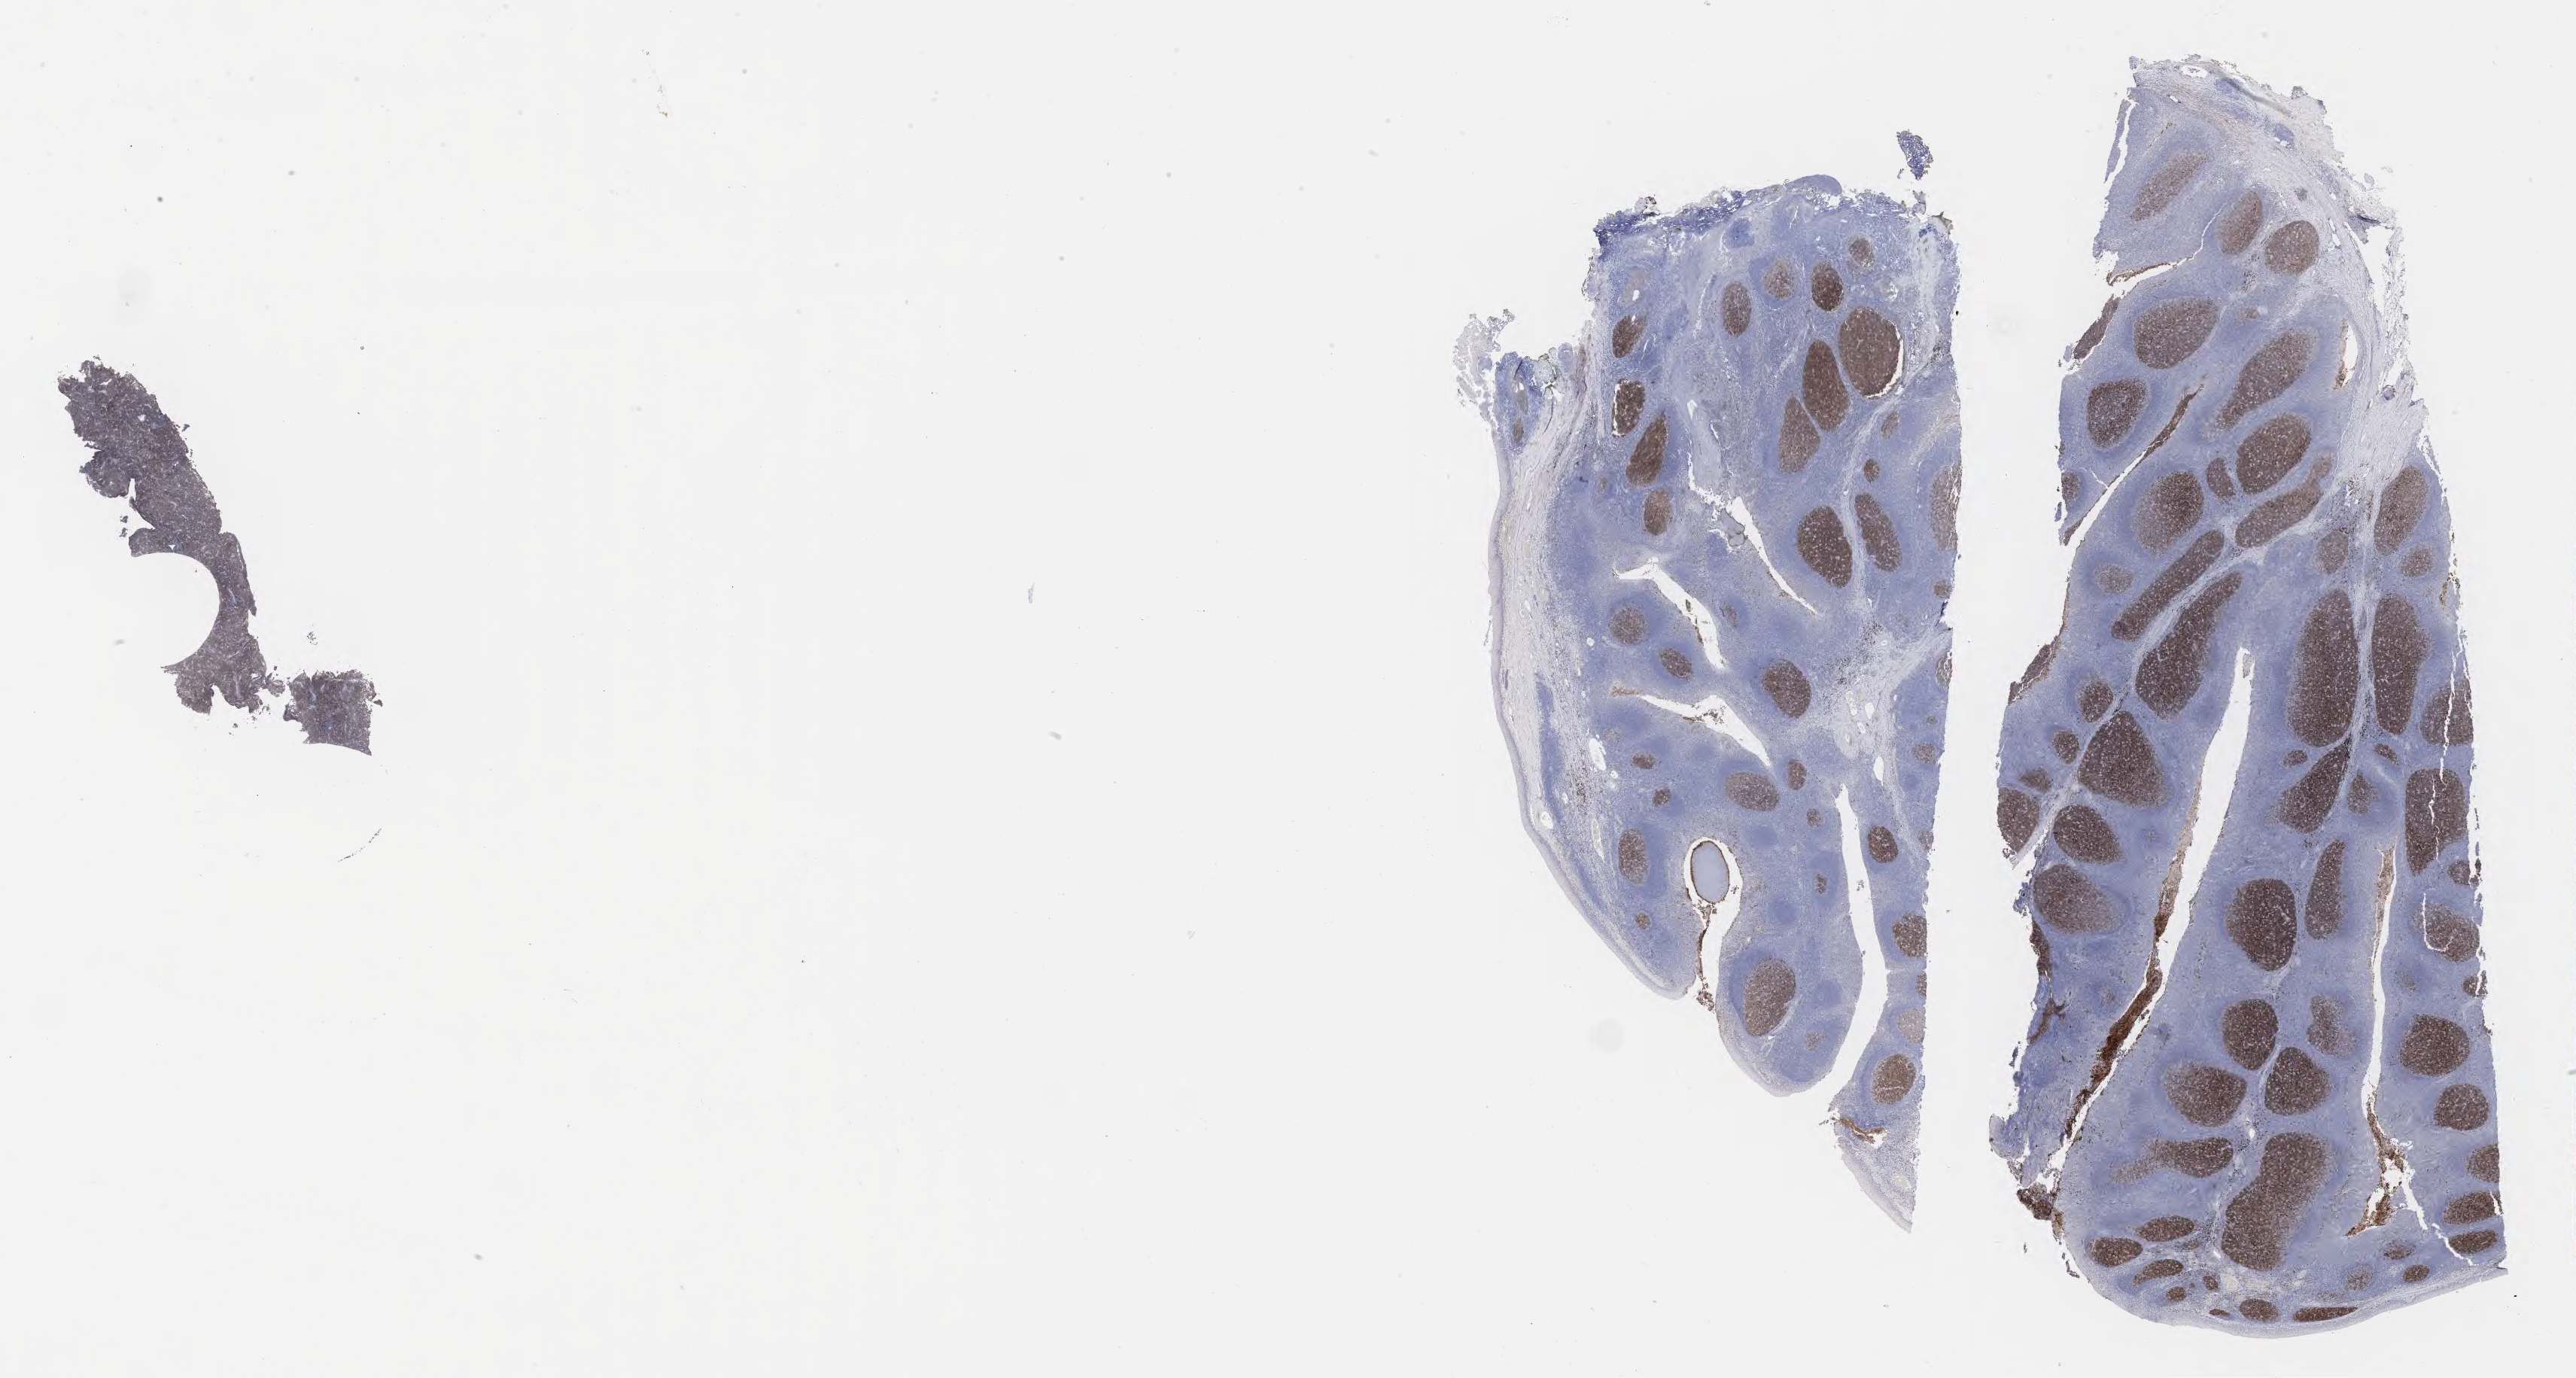
IHC for CD10, whole-slide image, shown as a low-resolution overview of the whole scanned area (about 27.7 x 14.8 mm), specimen: tumor tissue. Male patient; age at initial diagnosis 5 years.
Histologic diagnosis: Burkitt lymphoma, NOS.